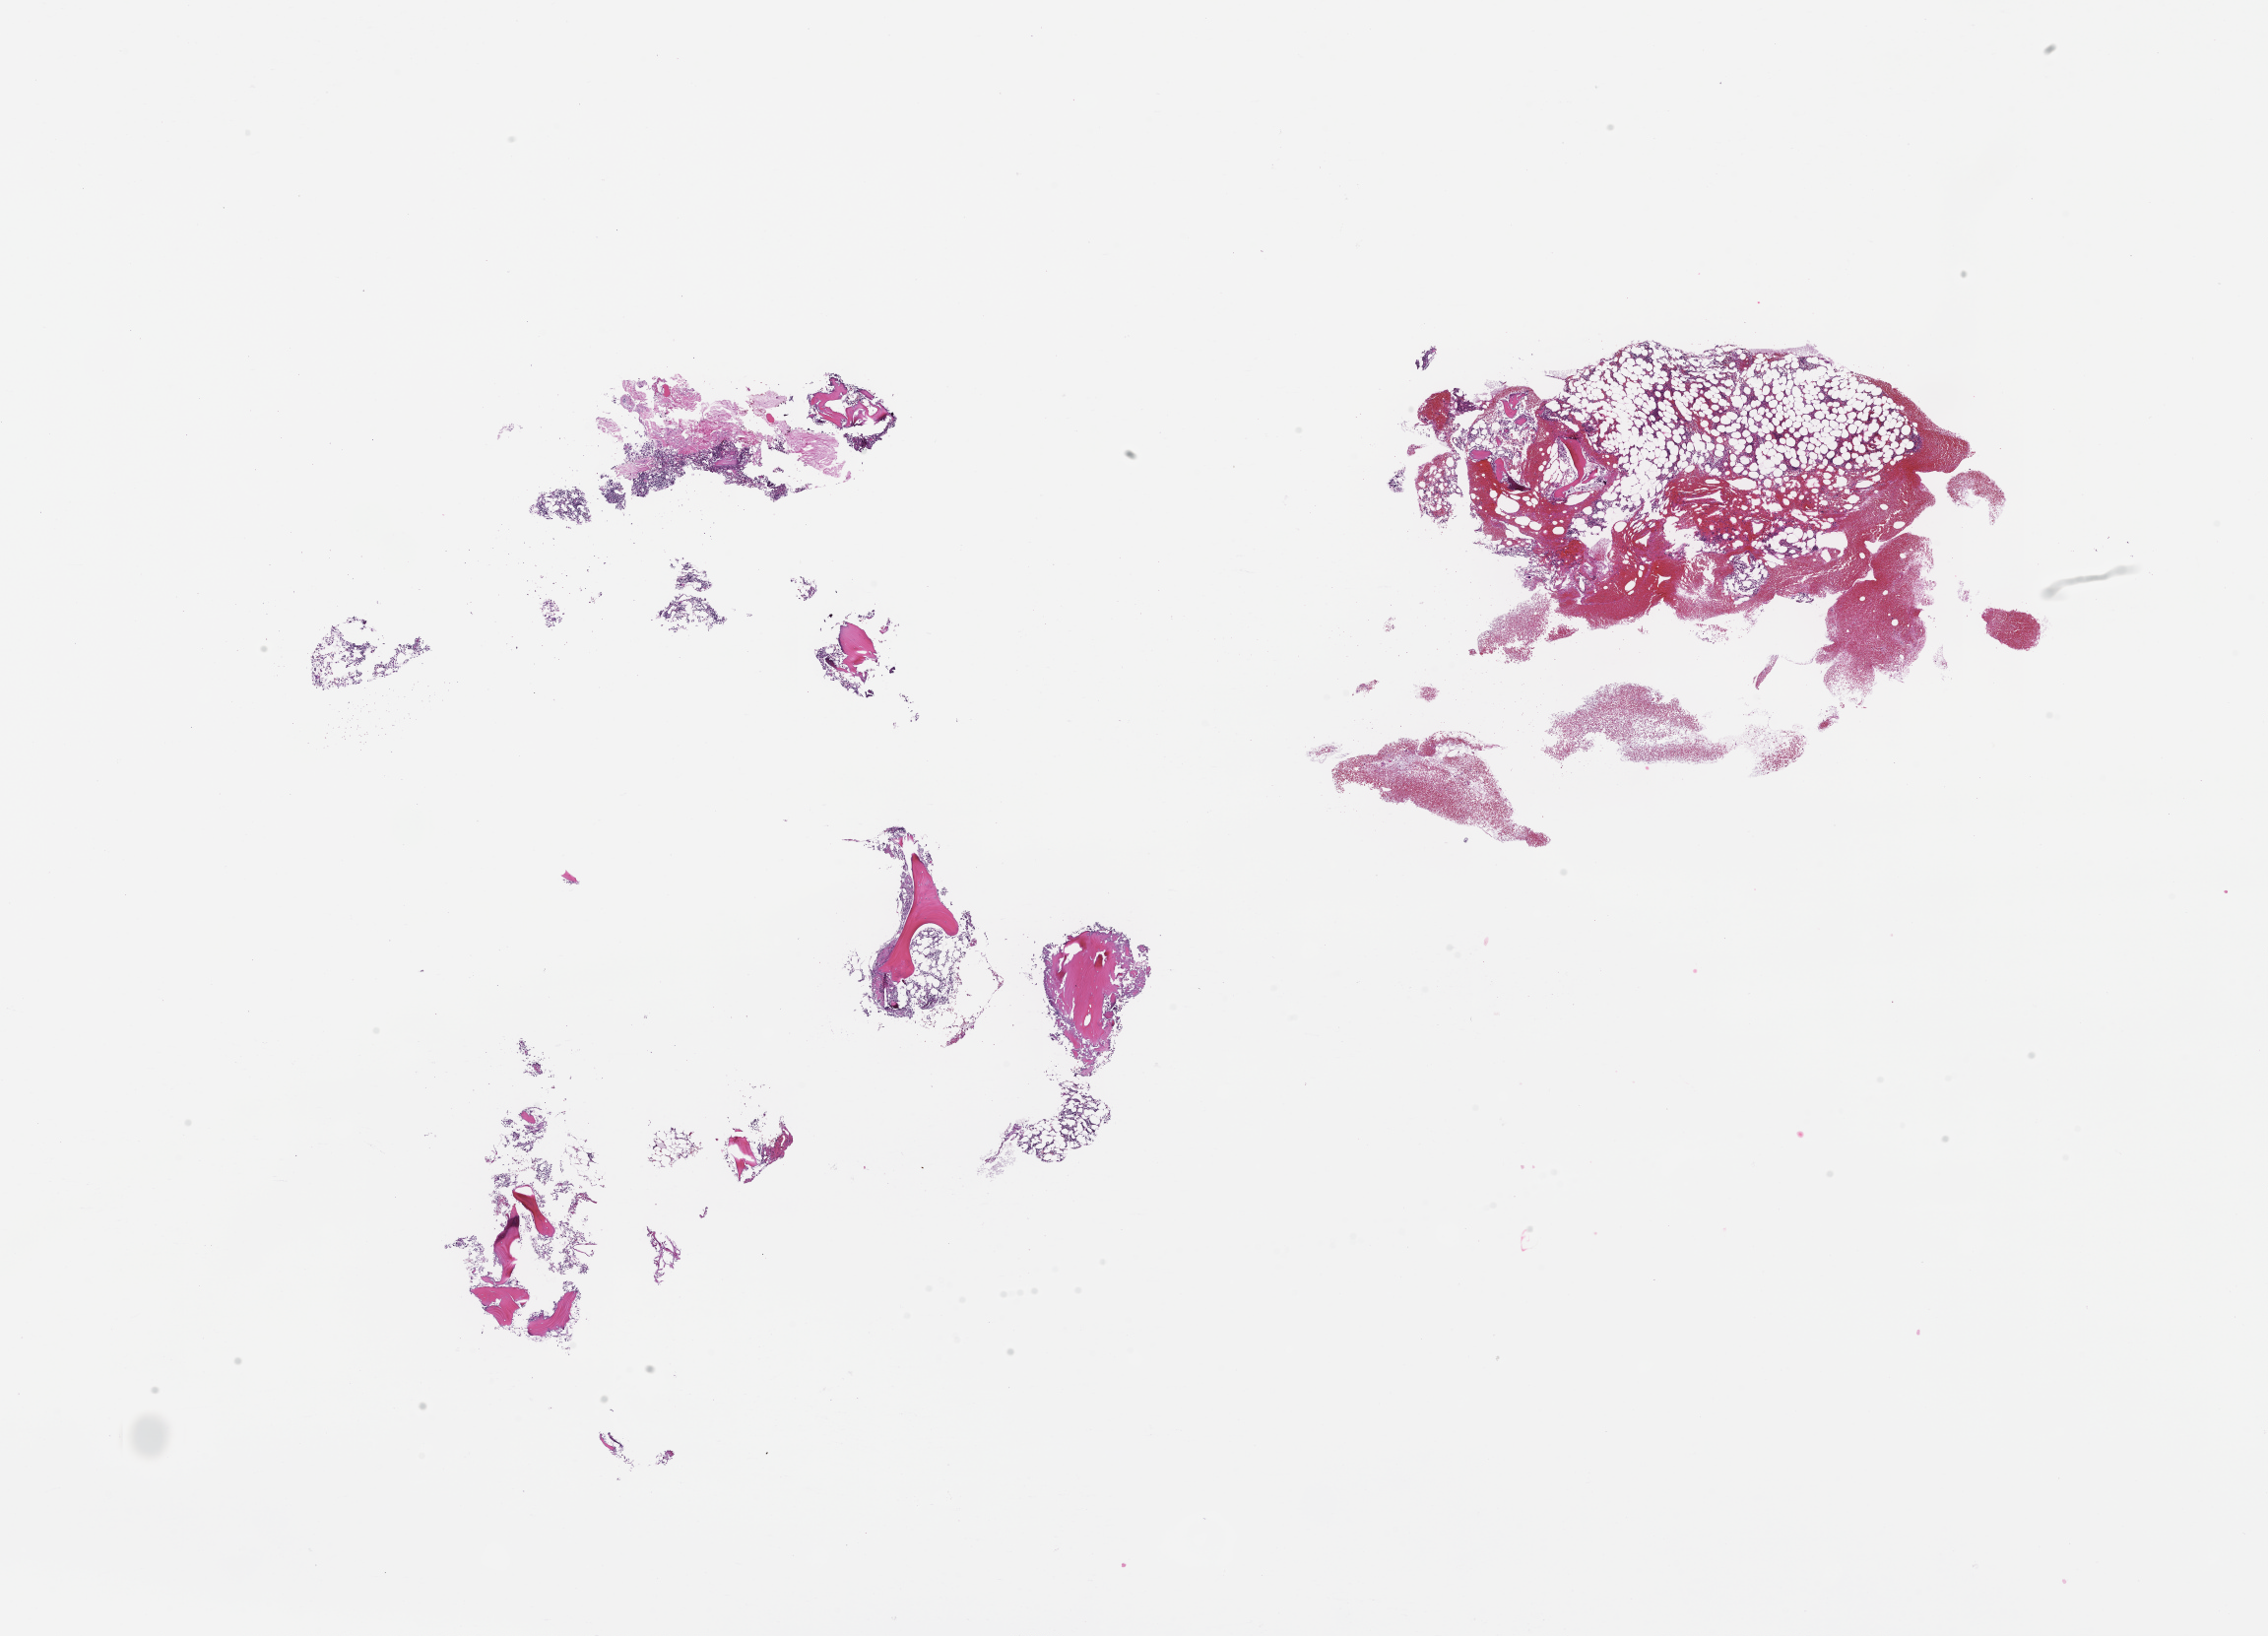
Haematoxylin and eosin whole-slide image, shown as a low-resolution overview of the whole scanned area (about 18.6 x 13.4 mm). FFPE section. Tissue site: bone marrow. Specimen time point: collected at baseline (before treatment). Patient: female.
This section: primary tumor. Diagnosis: Plasma Cell Myeloma.